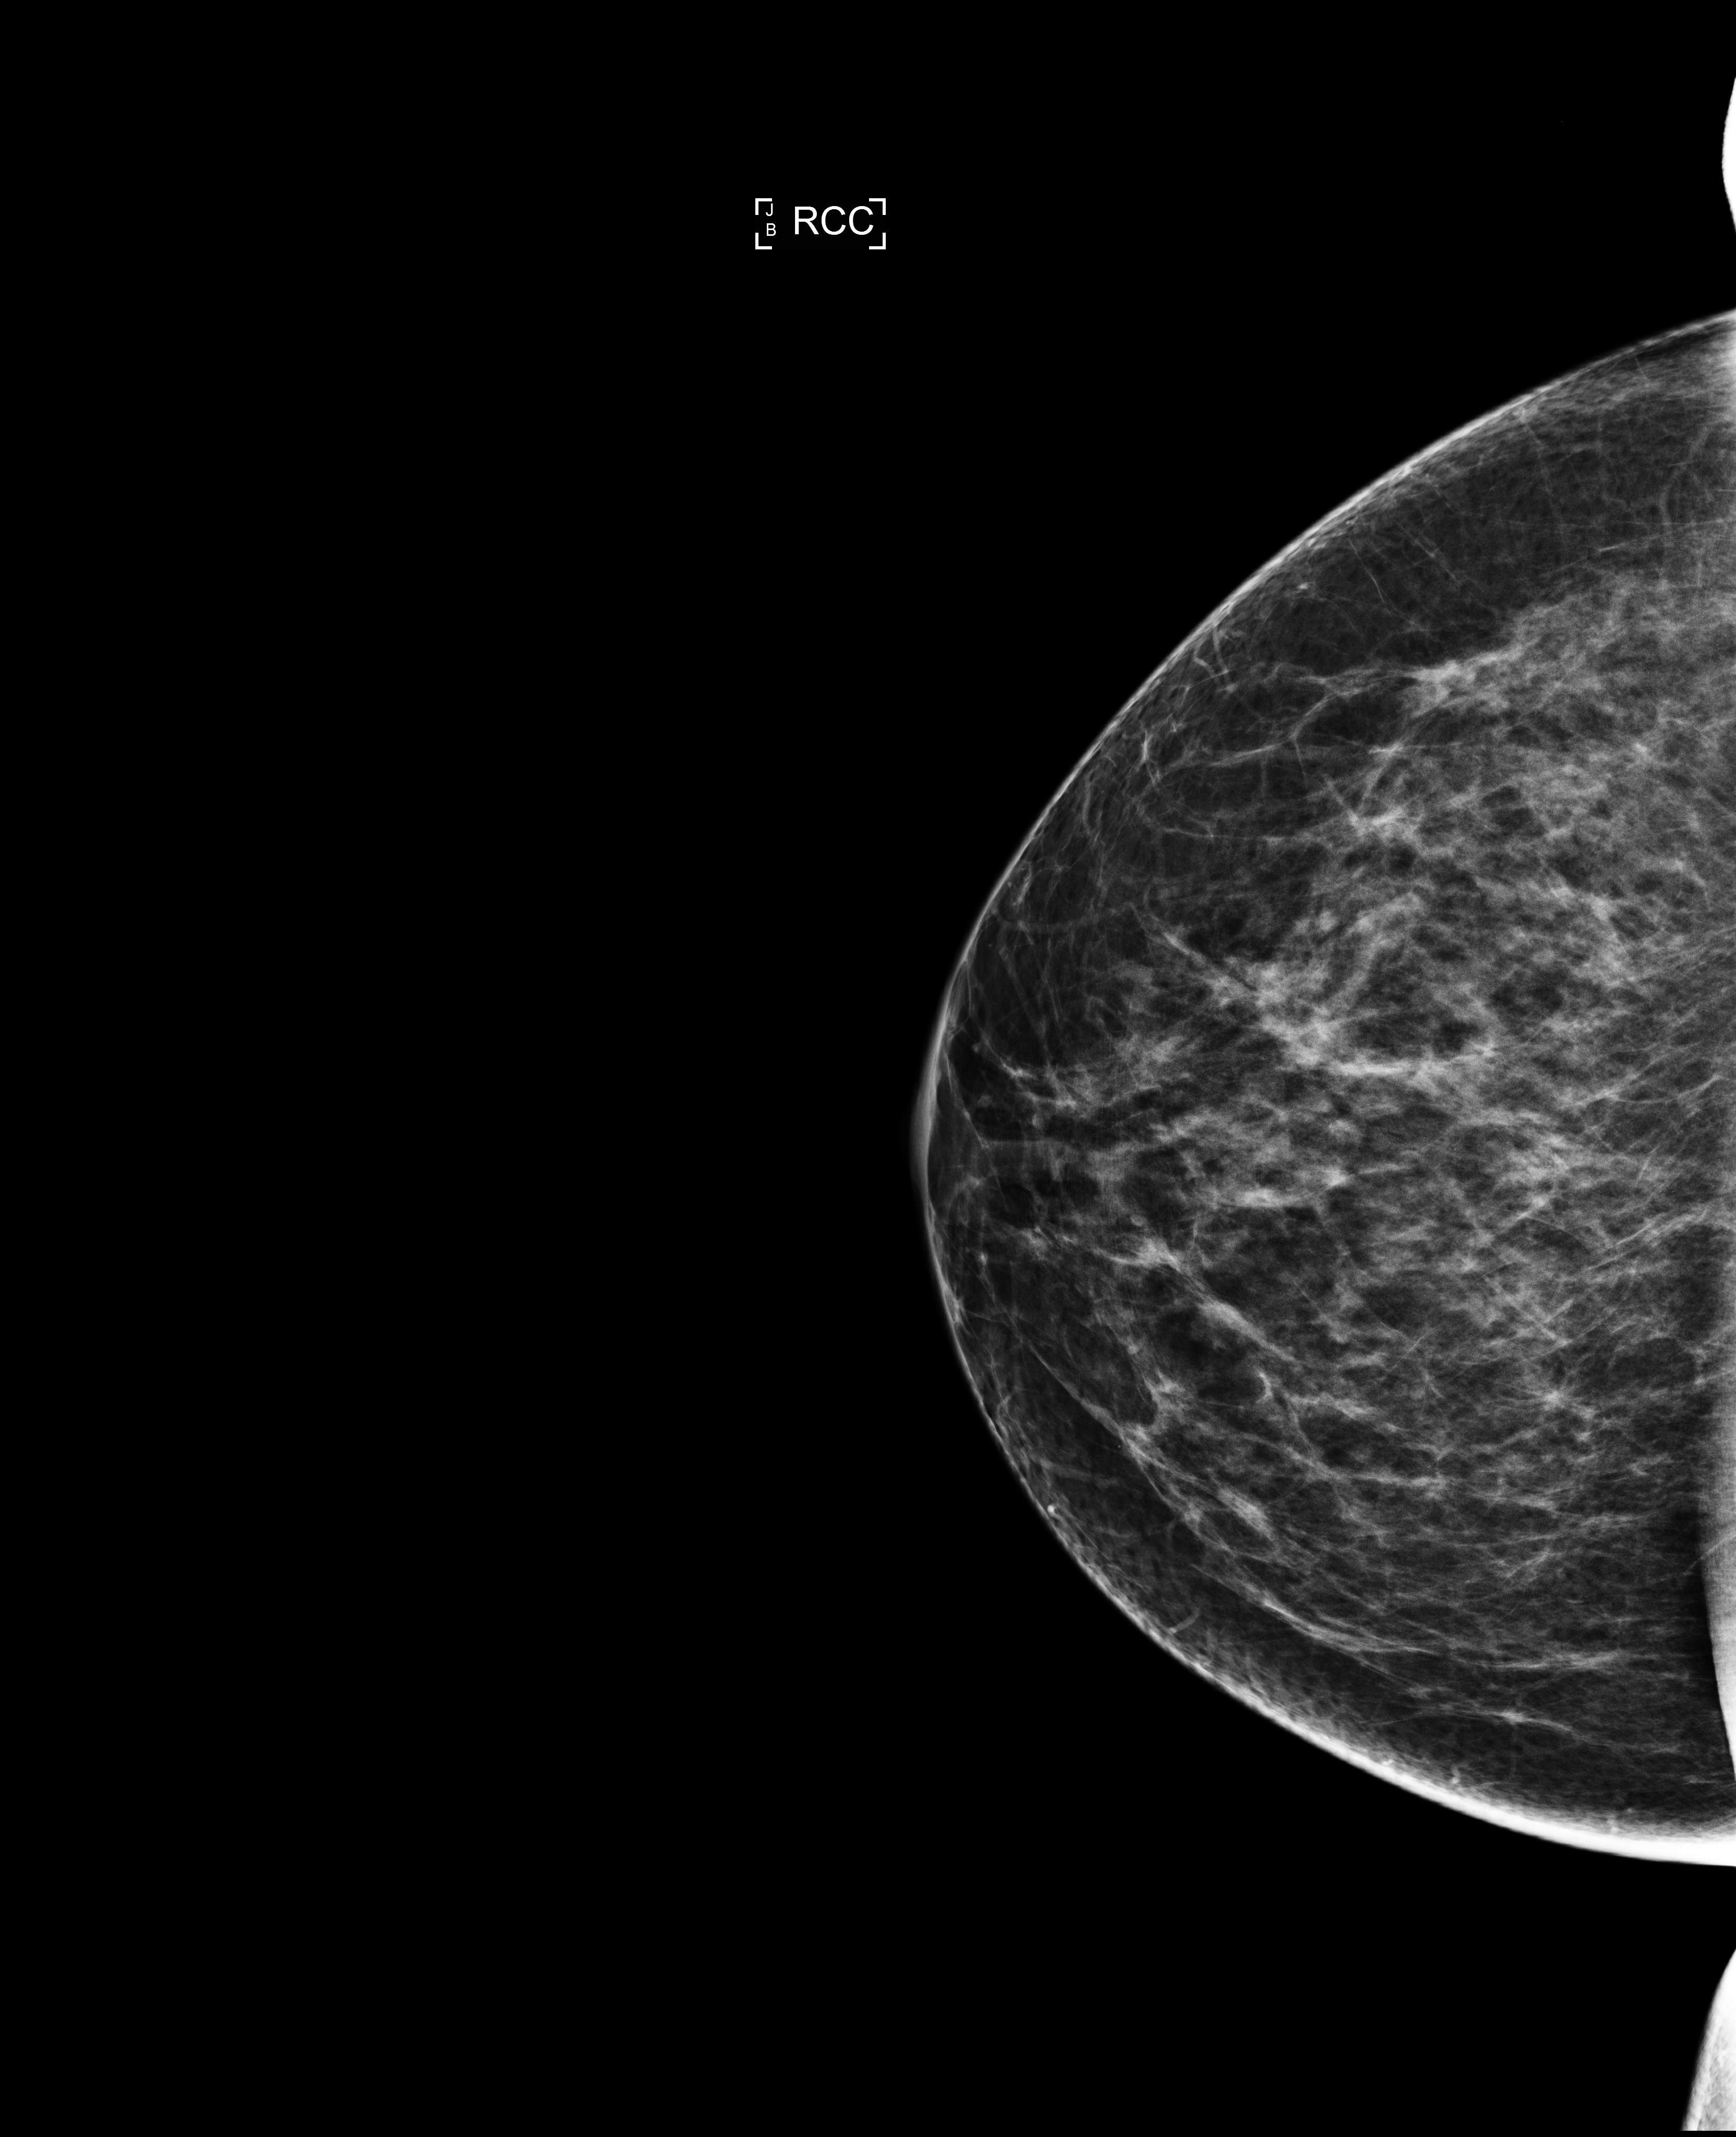
Screening examination, compressed breast thickness 81 mm, system: Selenia Dimensions.
Image type: full-field digital mammogram. Breast: right. Projection: CC view.